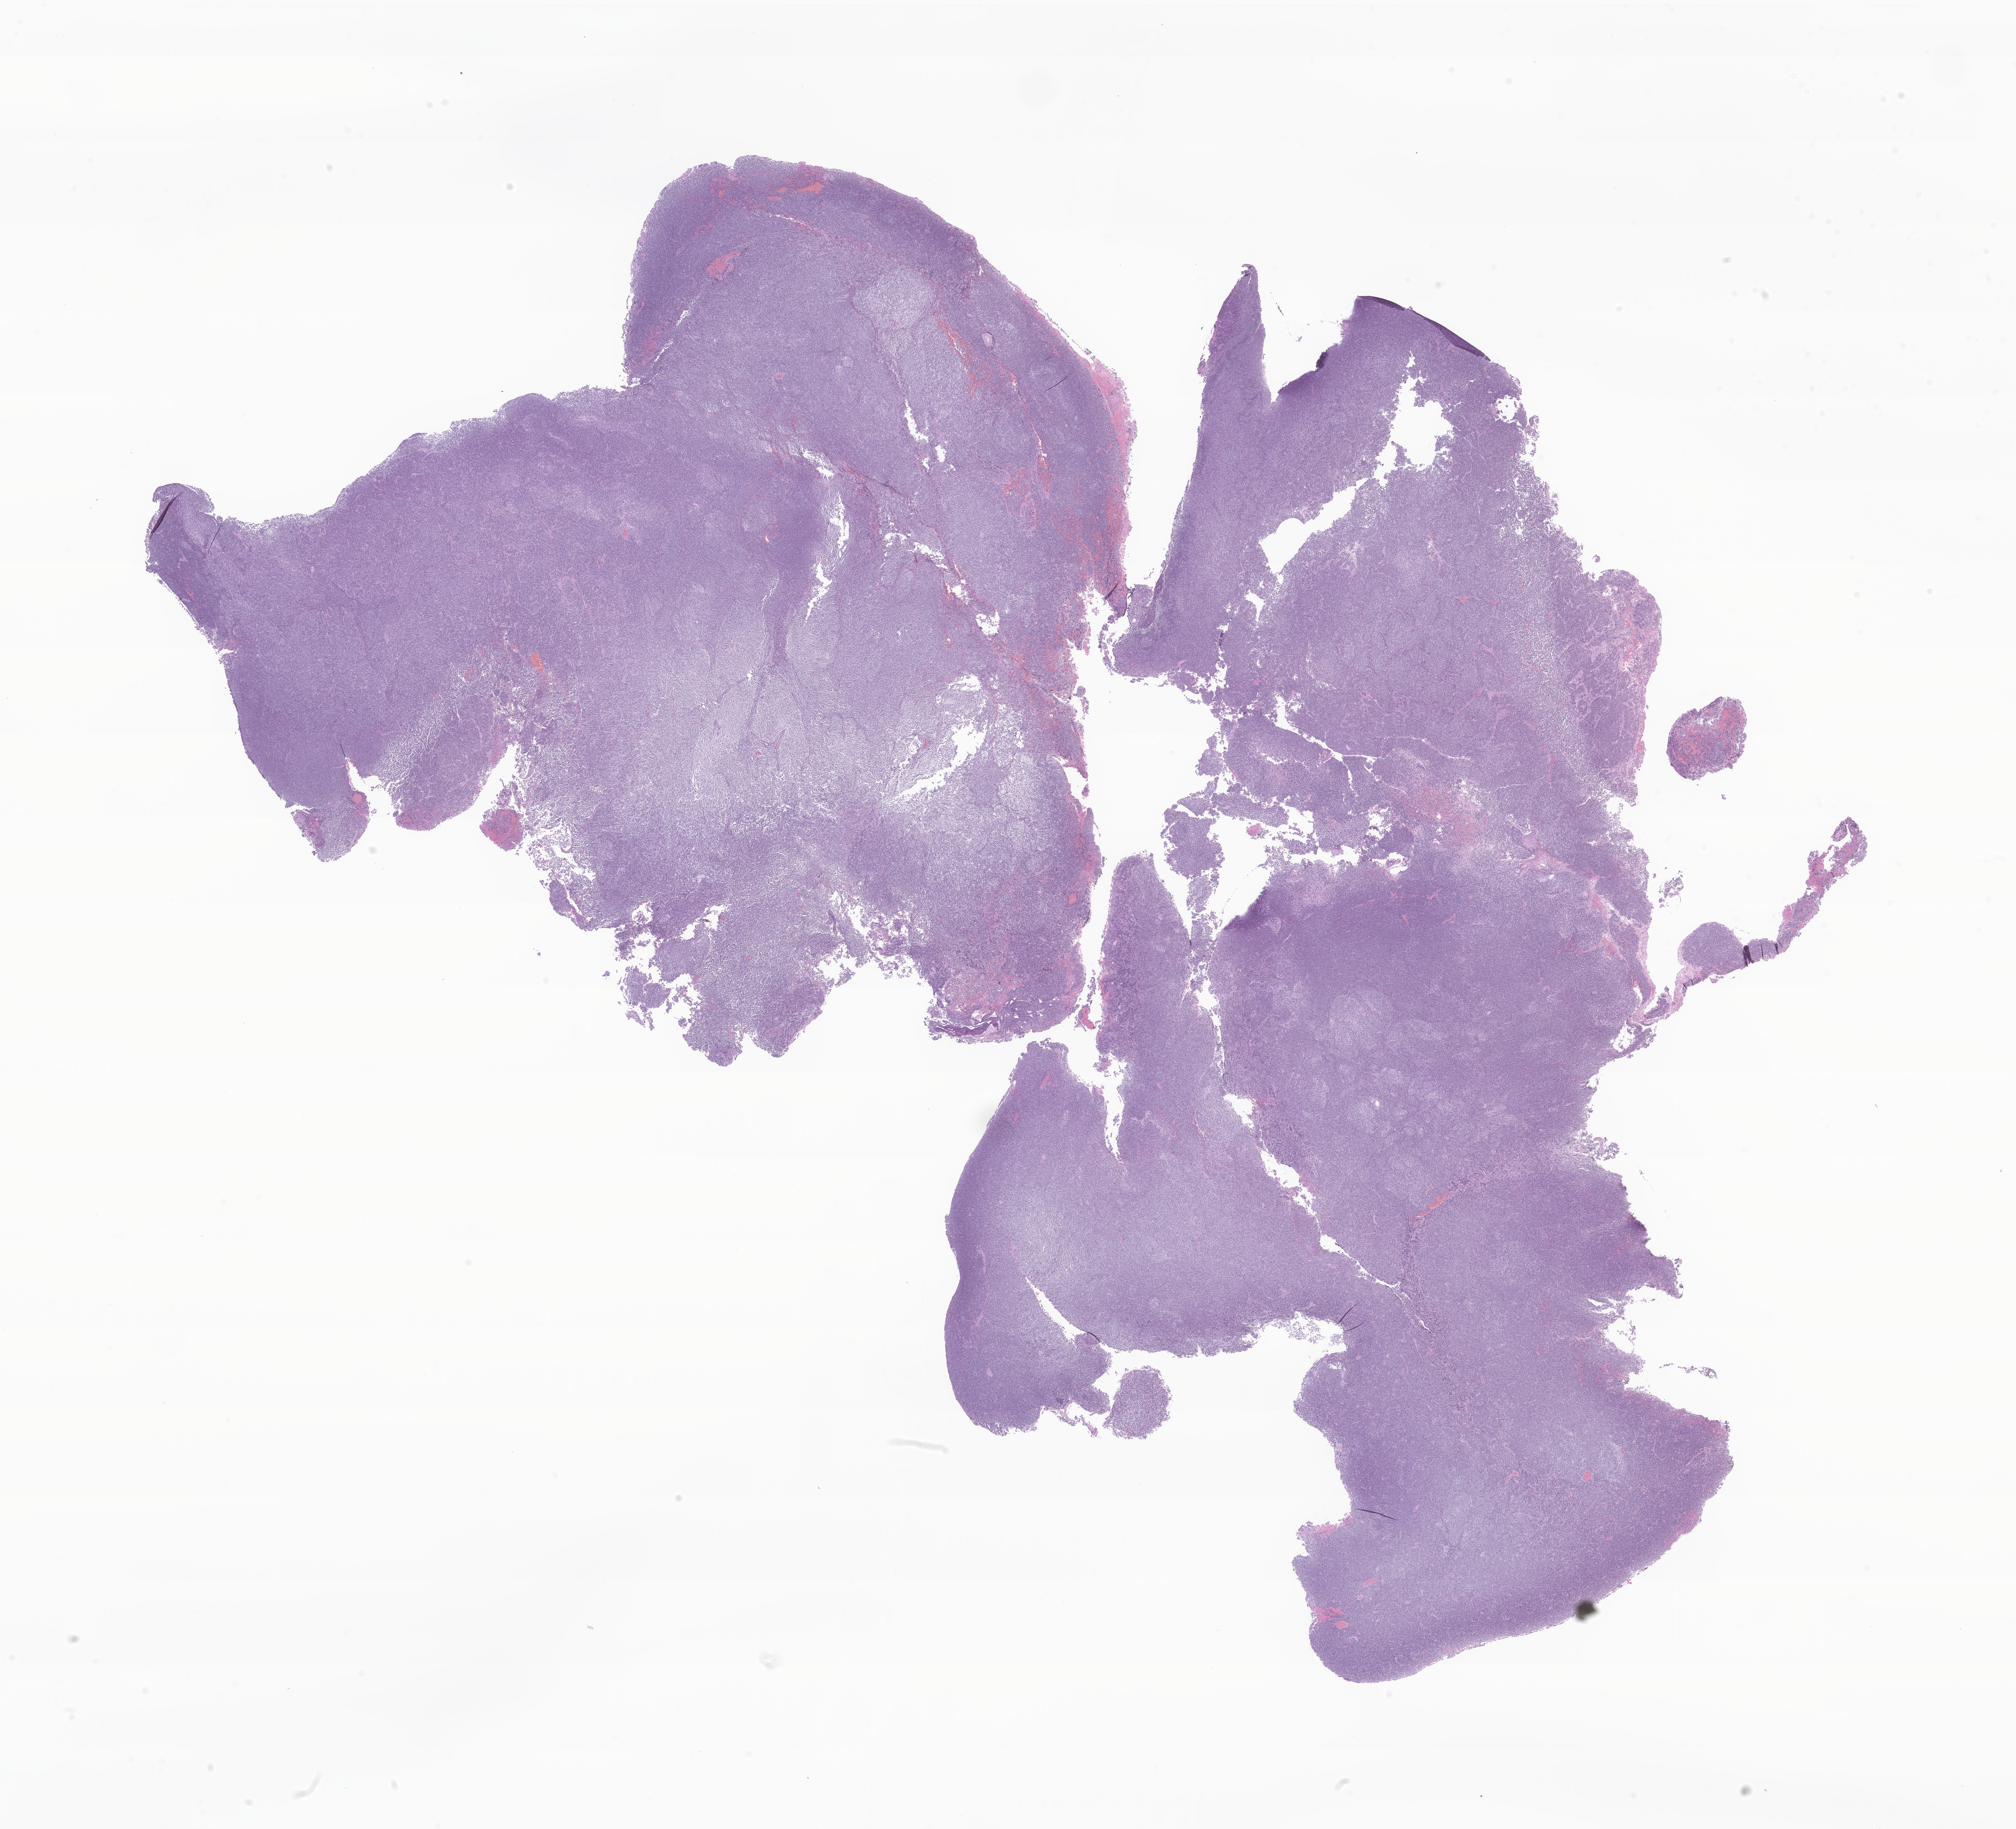
Digitized H&E-stained section of tumor tissue from the cerebellum — low-resolution overview of the scanned area, about 25.4 x 23.1 mm, formalin-fixed, paraffin-embedded (FFPE) tissue. Patient: female, age 106 months (8 years 10 months).
Diagnosis (ICD-O-3 morphology term): Medulloblastoma, NOS.